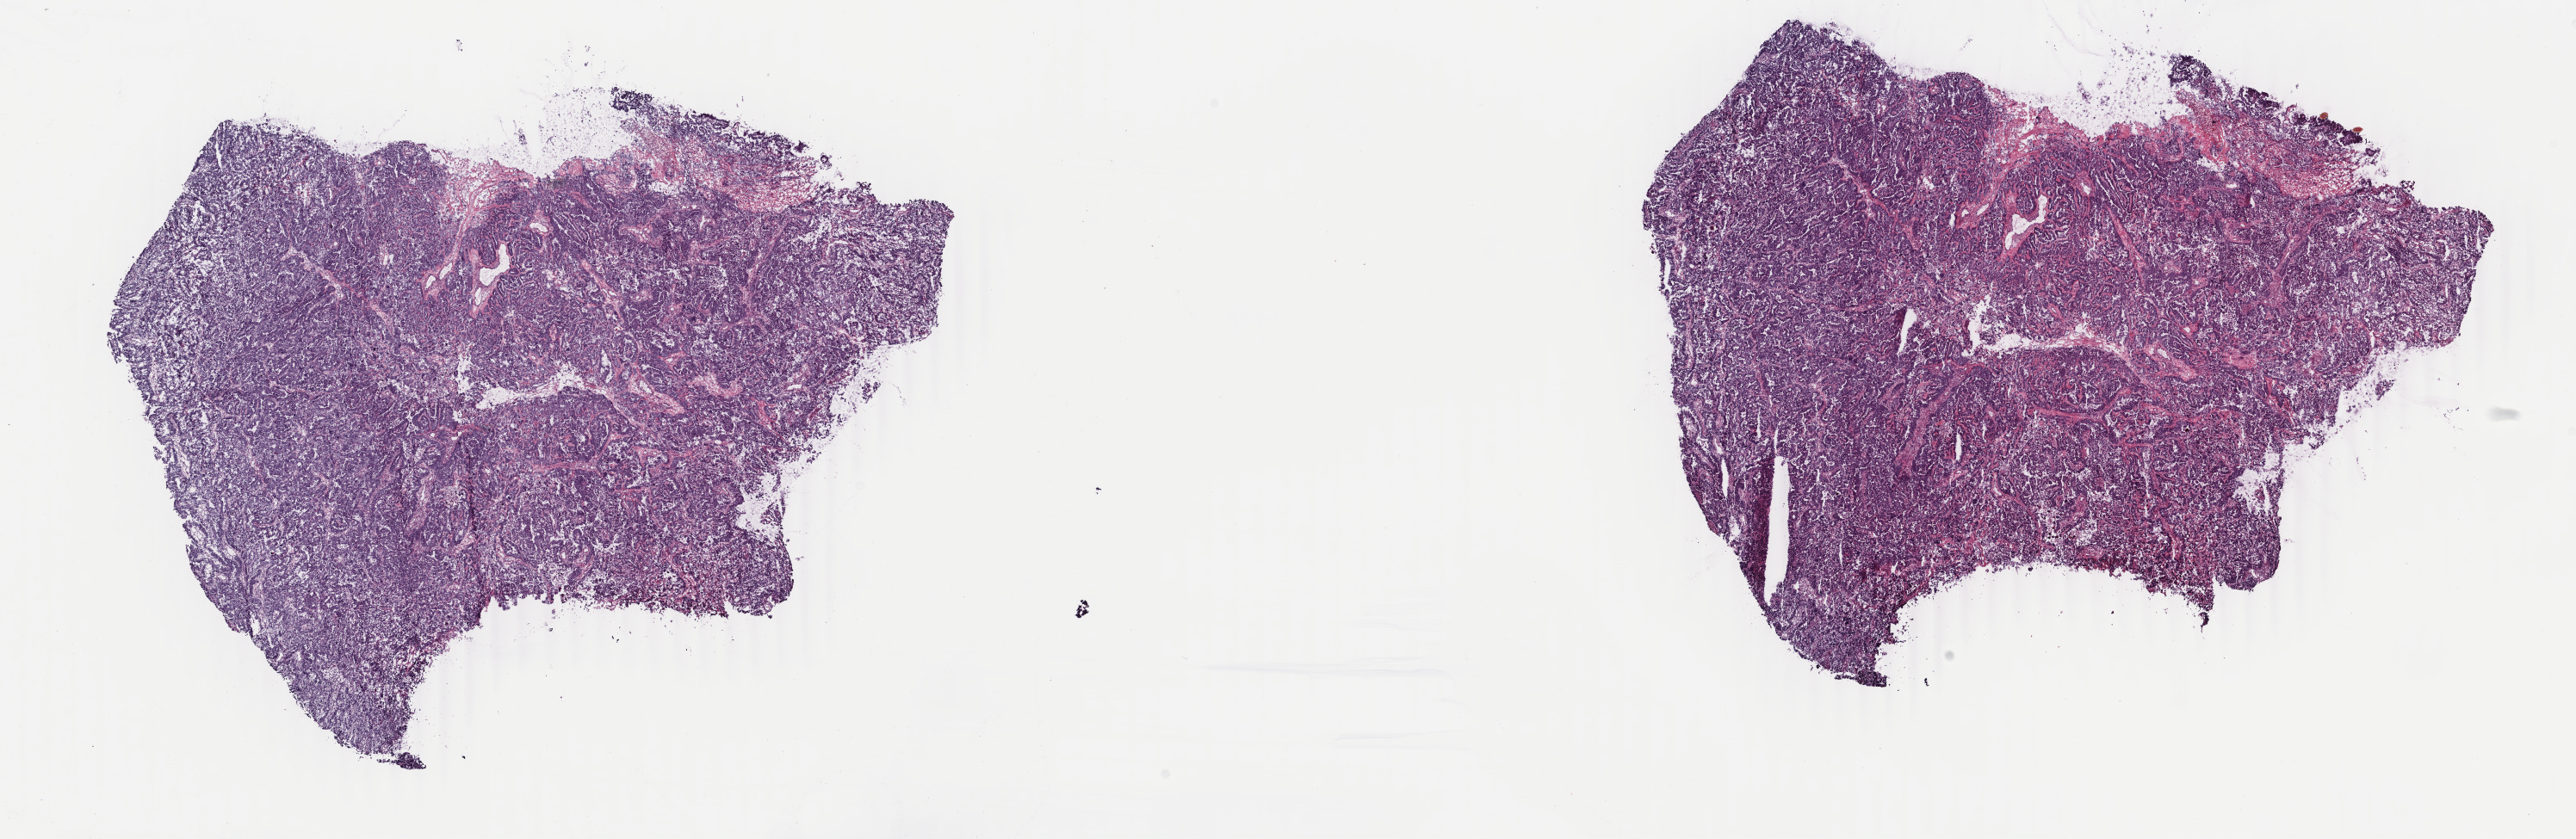
H&E-stained whole-slide image, a low-resolution overview of the entire scanned area, about 23.8 x 7.8 mm (from a 40x scan), frozen section, primary tumour sample from the uterus. Female, age 69 years at initial diagnosis. Composition of this section per pathologist review: tumour cells 90%, tumour nuclei 90%, normal cells 0%, stromal cells 0%, necrosis 10%. Inflammatory infiltration, as recorded: lymphocyte infiltration 20%, monocyte infiltration 20%, neutrophil infiltration 40%.
- pathologic diagnosis: Mullerian mixed tumor (endometrium)
- lymph nodes positive (case pathology): 0 of 5 examined
- FIGO stage: IA